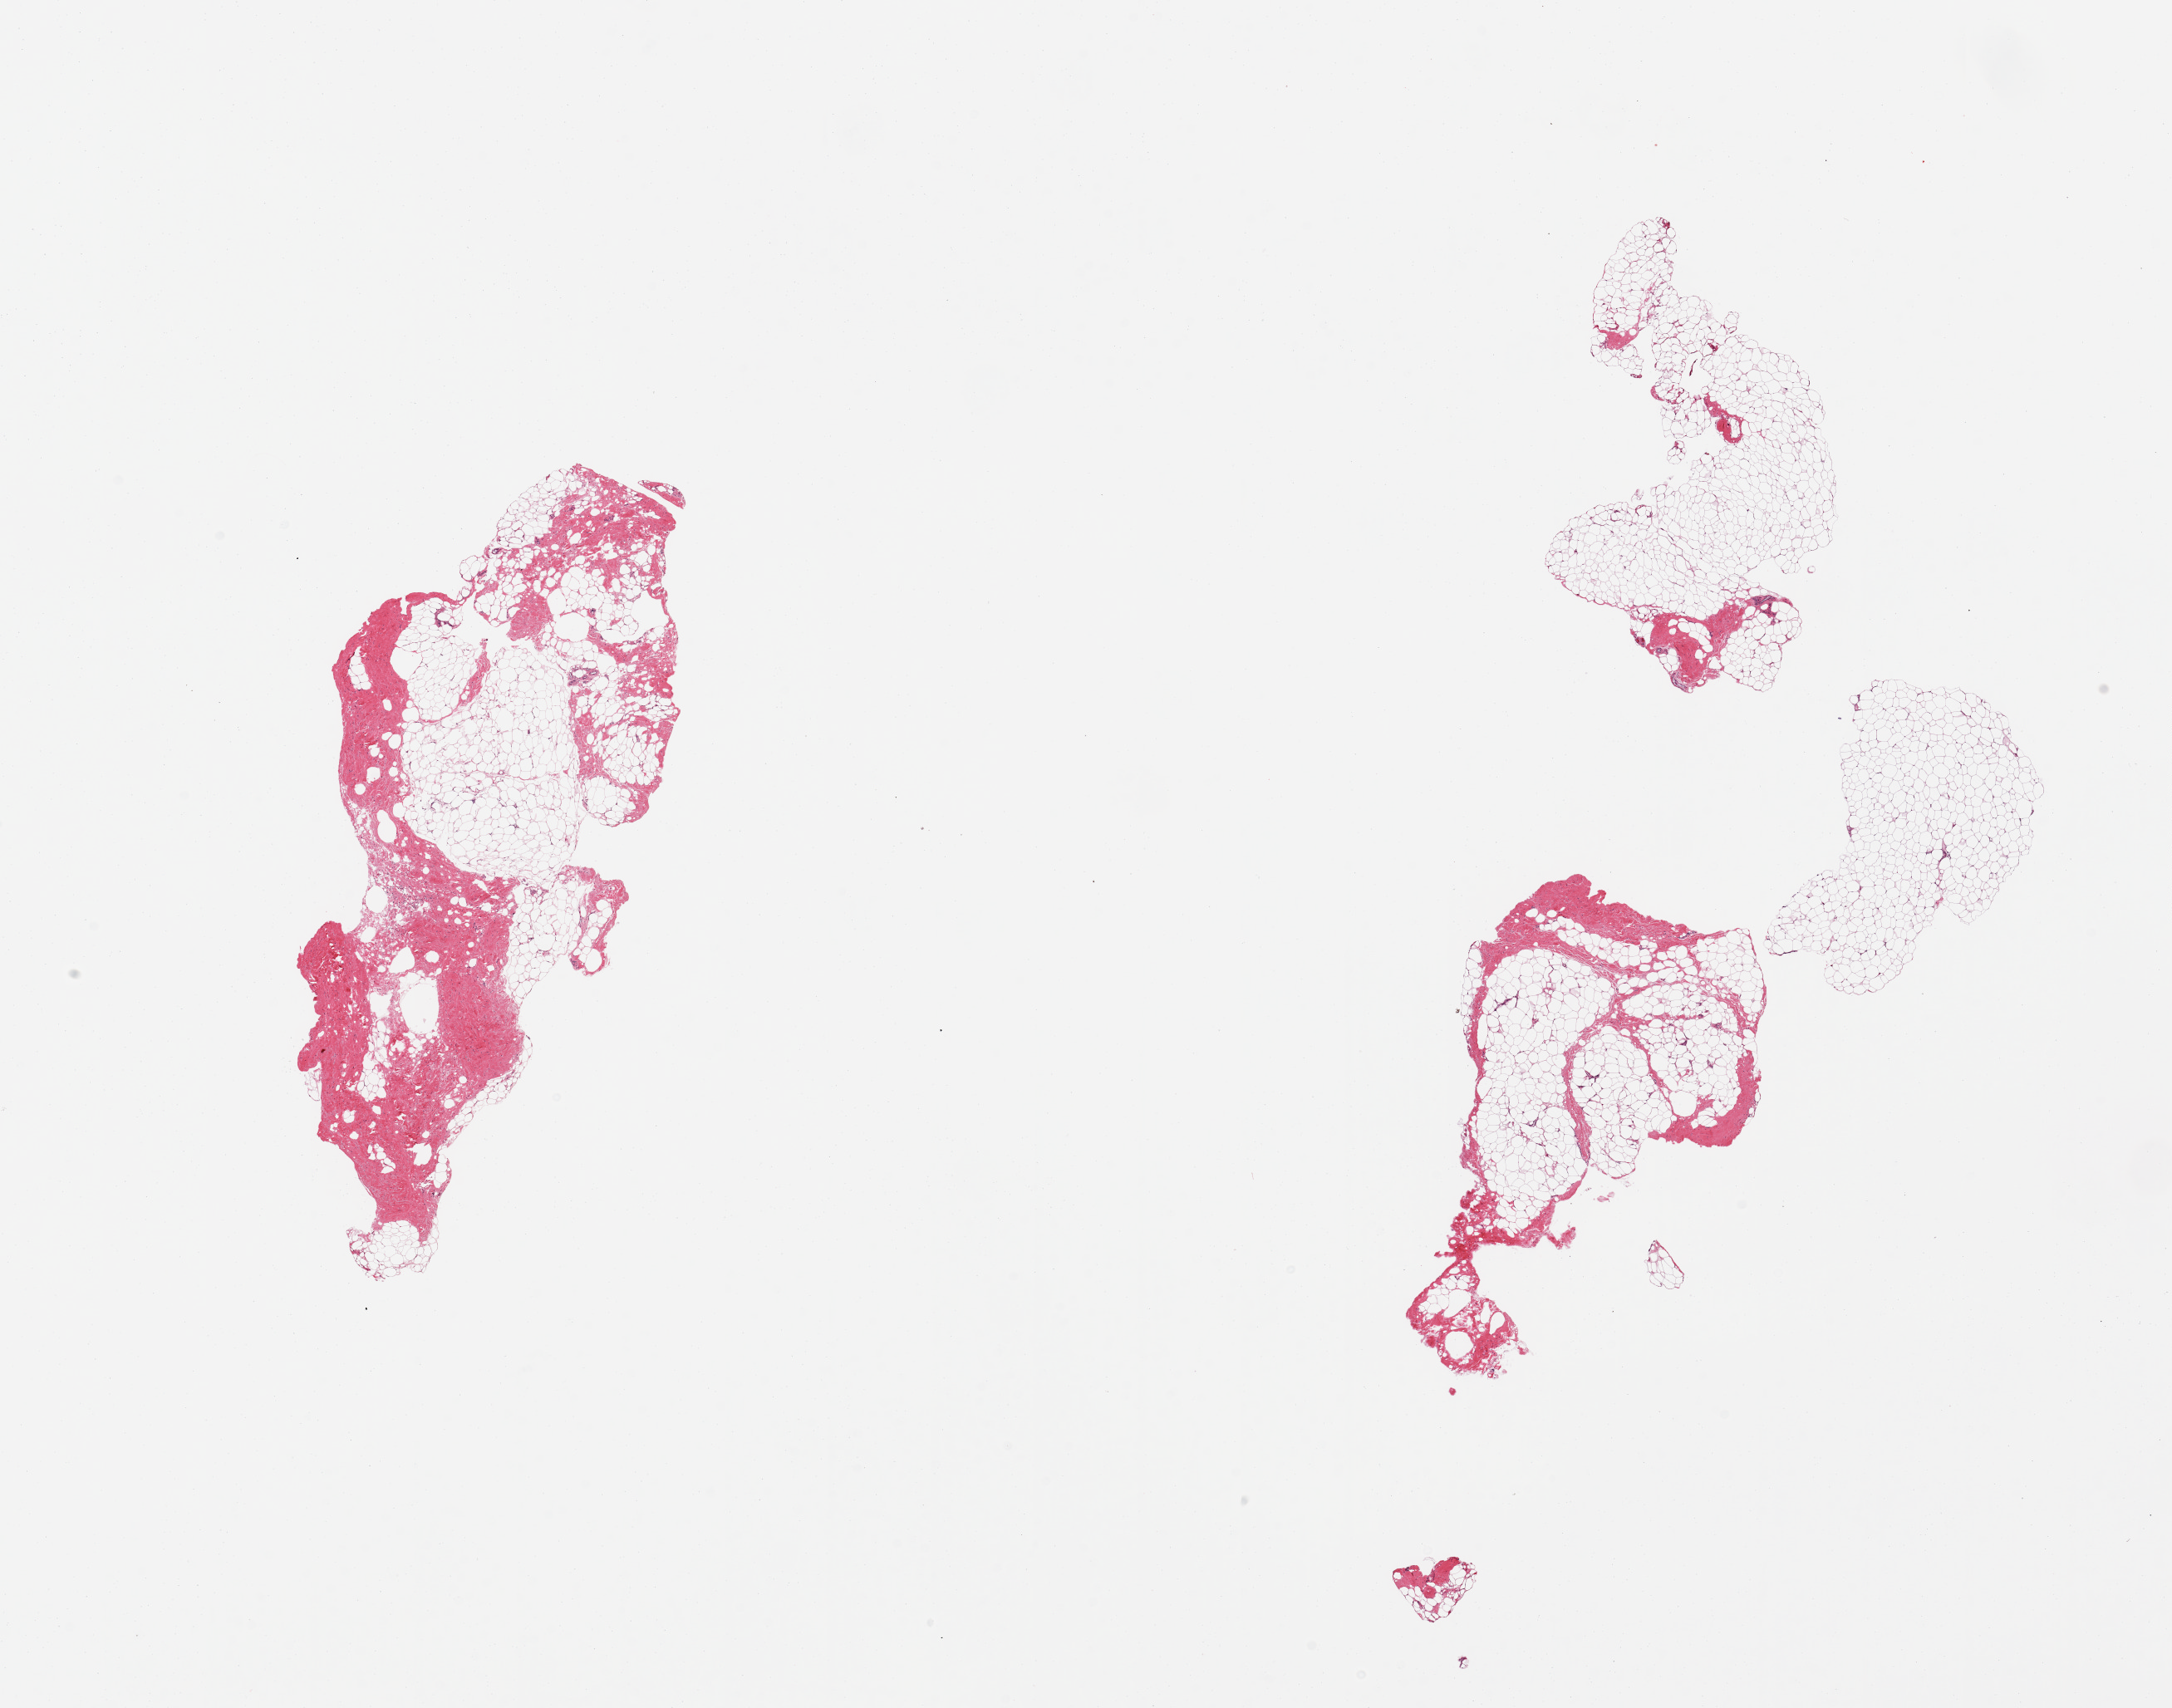
Hematoxylin and eosin (H&E) whole-slide image — whole scanned area (about 20.7 x 16.3 mm) shown as a low-resolution overview; PAXgene-fixed paraffin-embedded (PFPE) section; sampled site (target tissue): breast; tissue donor sample.
Reviewer comment on this tissue sample: 2 pieces; adipose tissue and stroma with no ductal structures observed.